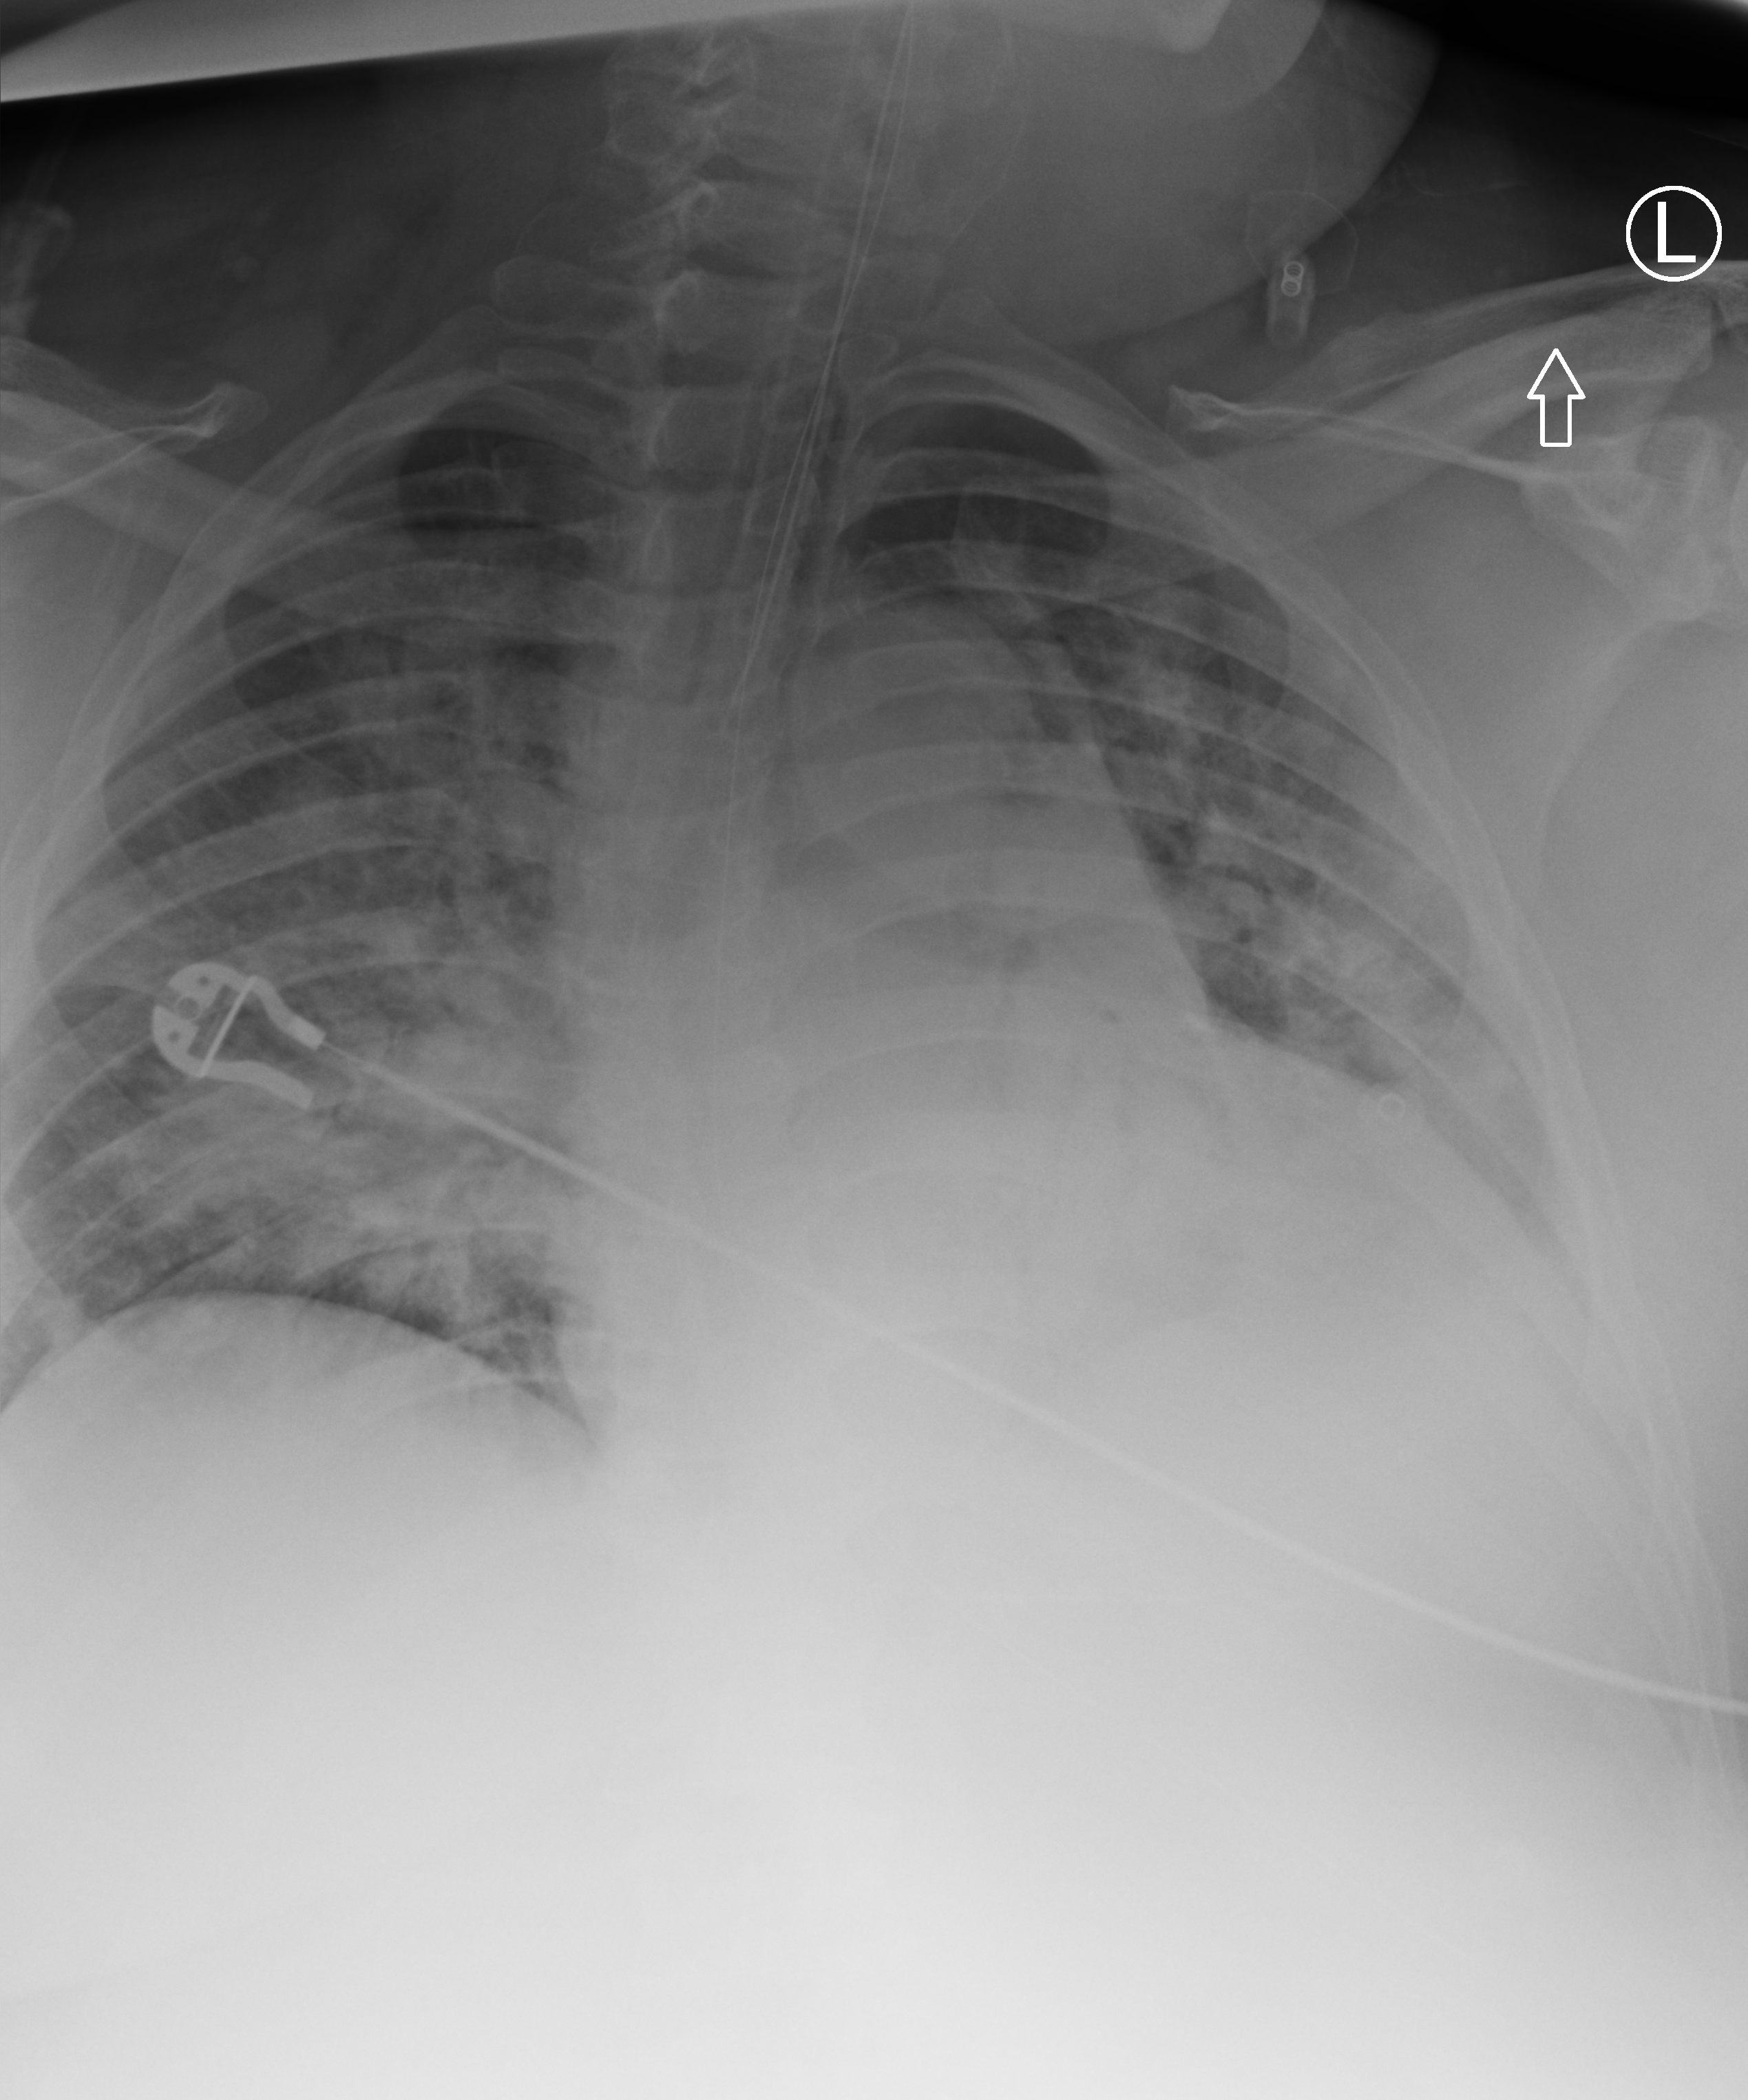
Portable chest radiograph; anteroposterior (AP) projection. Patient hospitalised with COVID-19; male, aged 18–59 years.
Admission-level facts for this patient (not findings on this image; timing relative to this image not recorded):
- other chronic lung disease (admission record): no